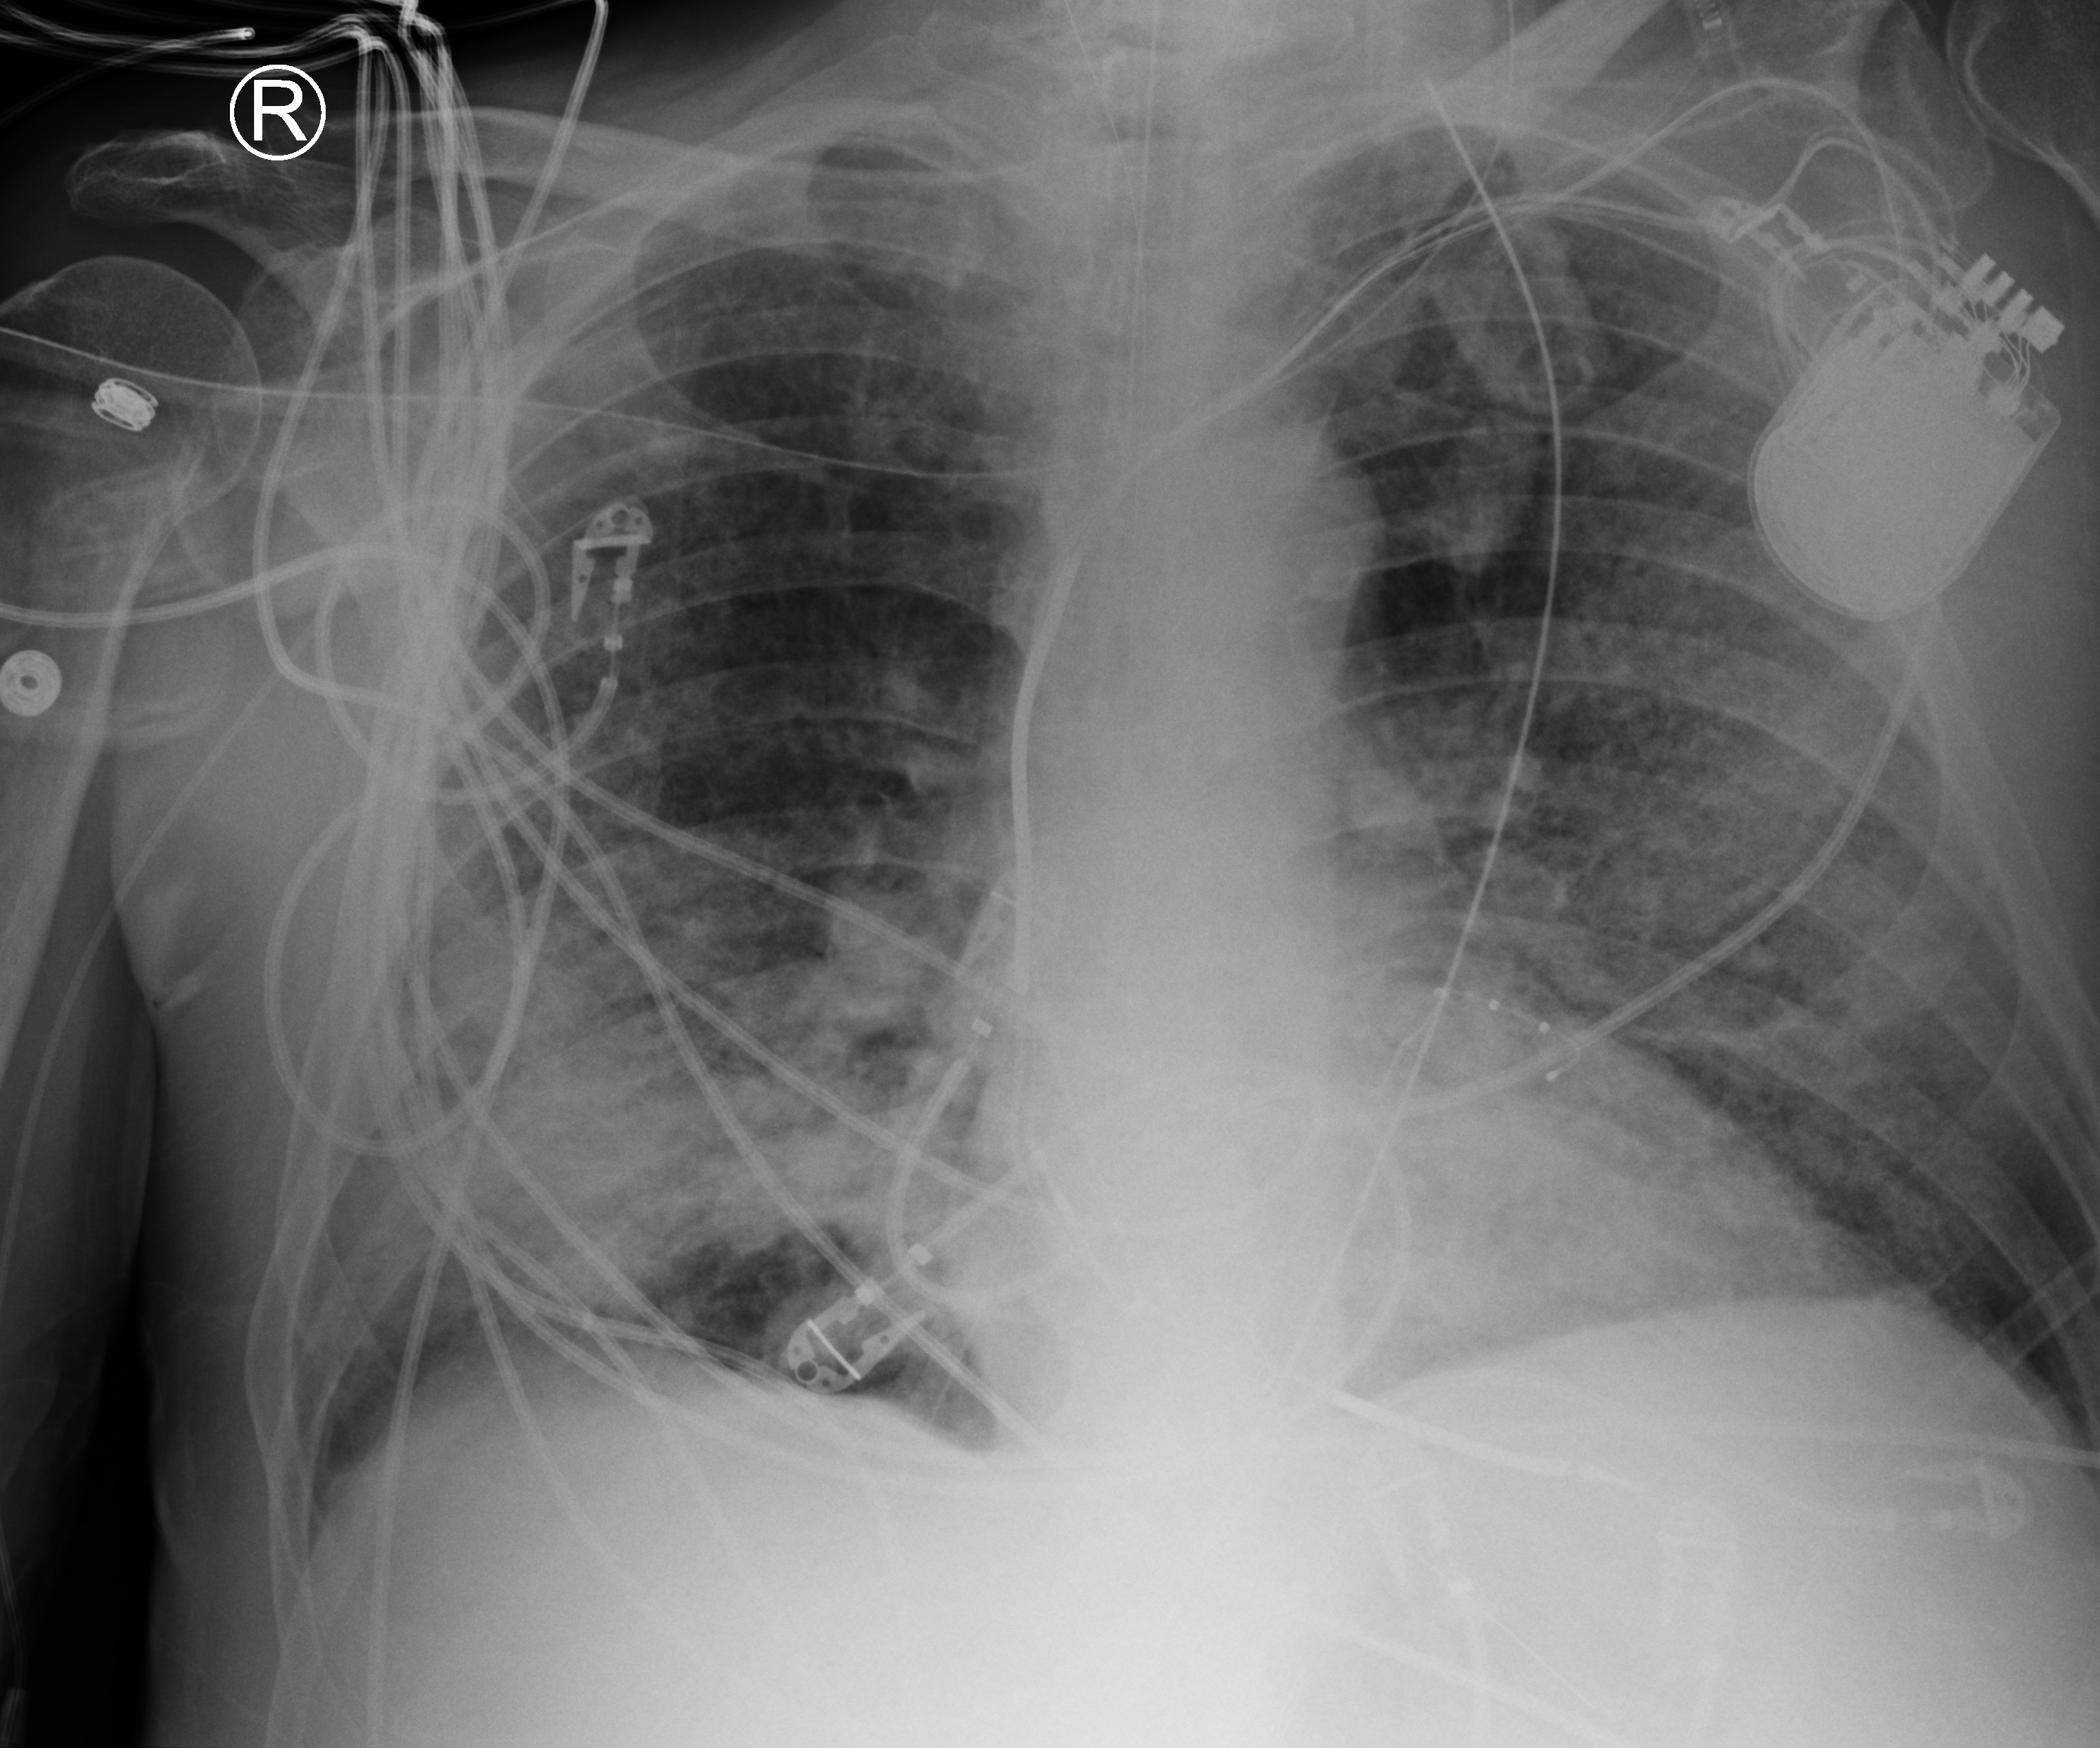
Bedside chest radiograph (computed radiography), anteroposterior (AP) projection. Patient hospitalised with COVID-19; male, aged 60–74 years.
From the hospital-stay record, not from the radiograph (when in the stay this image was taken is not recorded):
- other chronic lung disease (admission record): no
- mechanically ventilated during this hospital stay: yes
- length of hospital stay: 36 days